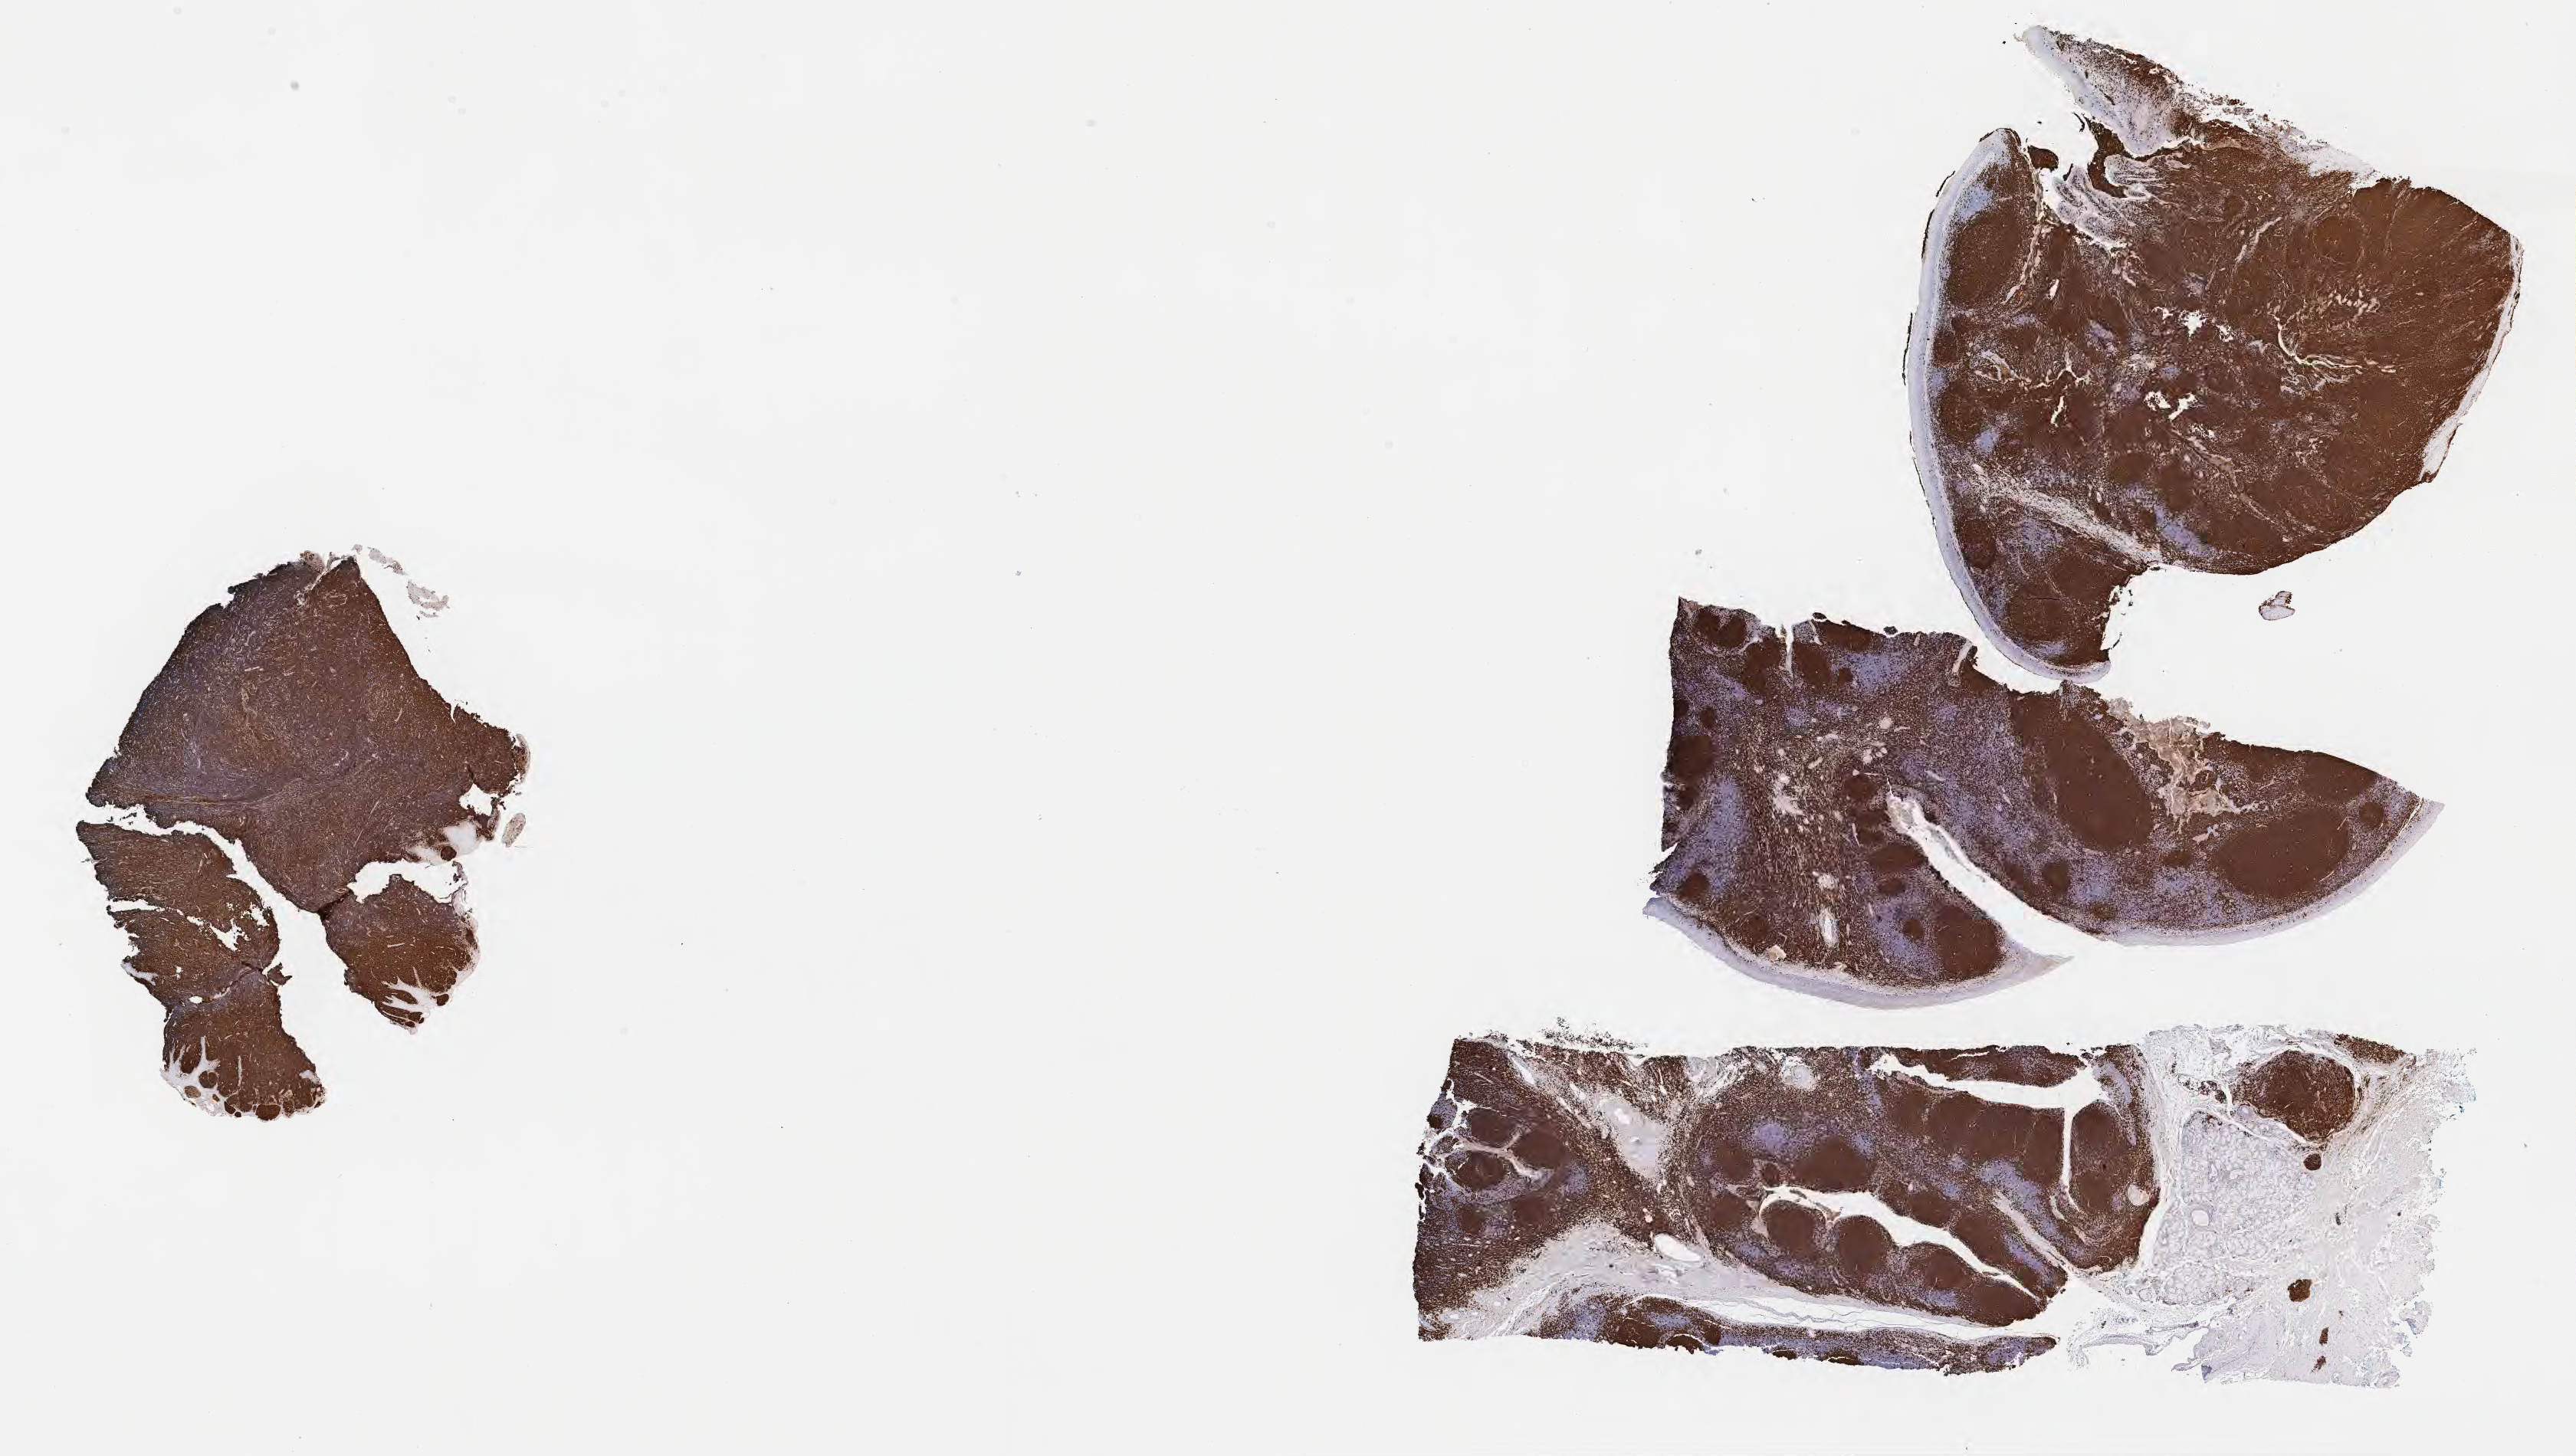
IHC for CD20, whole-slide image — whole scanned area (about 27.2 x 15.4 mm) shown as a low-resolution overview. Specimen: tumor tissue. Anatomic site: cranium. Male patient, 11 years old.
Histologic diagnosis: Diffuse large B-cell lymphoma, NOS.